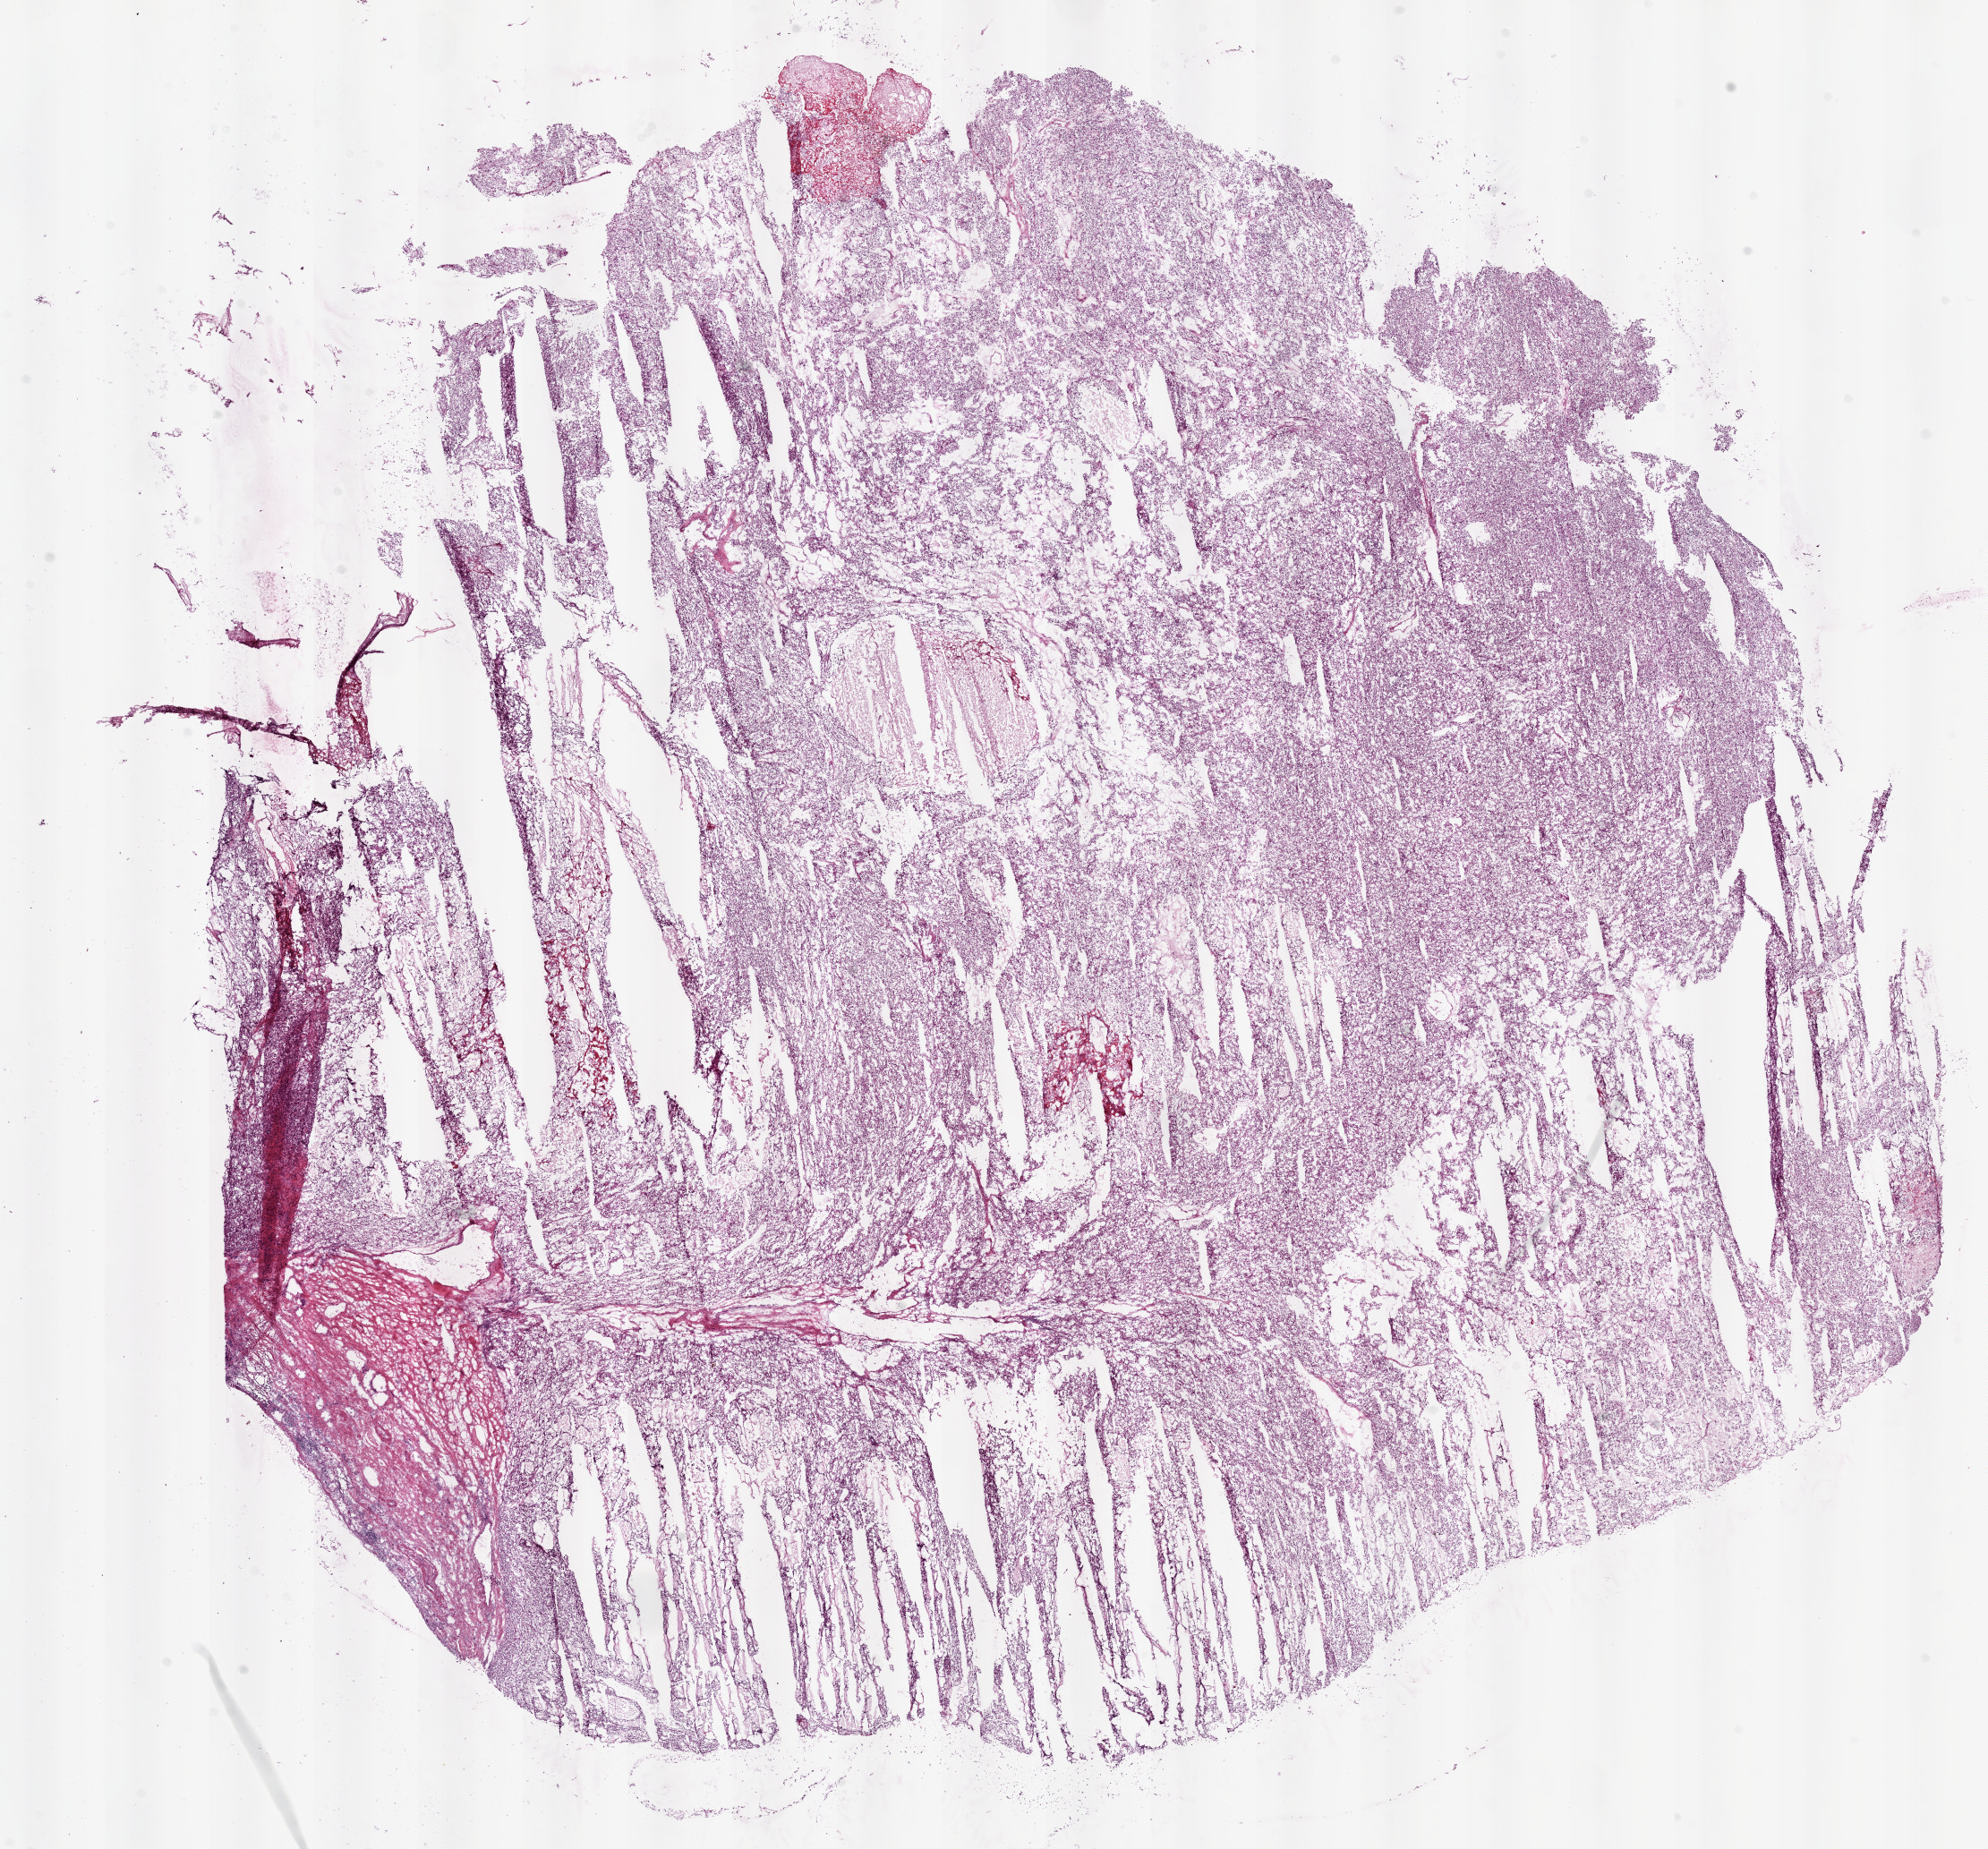
Digitized Hematoxylin and eosin (H&E) stained tissue section (whole slide), a low-resolution overview of the entire scanned area, about 17.8 x 16.6 mm (acquisition: 5x scan). Frozen section. Sample: primary tumour, kidney. Female patient; age at initial diagnosis 72 years. Histologic grade: G4 (undifferentiated). Slide review estimates, as recorded: tumour cells 95%, tumour nuclei 85%, normal cells 0%, stromal cells 5%, necrosis 0%.
- histologic diagnosis: Clear cell adenocarcinoma, NOS
- laterality: left
- AJCC pathologic stage: III
- lymph nodes positive (case pathology): 0 of 5 examined